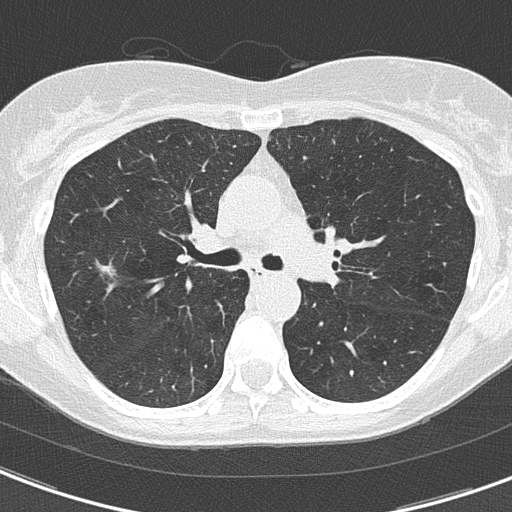
Low-dose screening chest CT, axial slice; second annual screen; lung window (W 1500 / L -600 HU); slice 57 of 156 in the series; 512 × 512 image matrix. Female participant, aged 59 years at enrolment. Current smoker at enrolment.
• Expert-annotated lung lesion, bounding box <81,250,138,293> (left, top, right, bottom; pixels).
• The exam's reader record, not a measurement of the box and not confirmed to be the same lesion: non-calcified nodule or mass ≥4 mm, right upper lobe, 7 × 6 mm, poorly defined margins, ground glass attenuation, pre-existing on the prior screen: yes; interval growth: no.
• Lung cancer was diagnosed 454 days after this screen: bronchiolo-alveolar adenocarcinoma, NOS, right upper lobe, well differentiated (G1), stage IA (AJCC 6th edition), 4 mm at pathology.